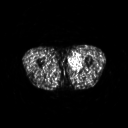
FDG PET of an extremity soft-tissue mass (from a PET/CT study), one axial slice; 3.27 mm slice thickness; 128 × 128 image matrix, field of view 500 × 500 mm. Patient: male, 29 years. From the clinical record (not read from this slice): histological type: mixoid liposarcoma; grade: low; site of the primary tumour: left thigh.
Structures marked on this image (expert contour drawn on MRI and transferred to this co-registered scan by the dataset authors):
- gross tumour volume (mass): box from (x=69, y=53) to (x=82, y=70) px